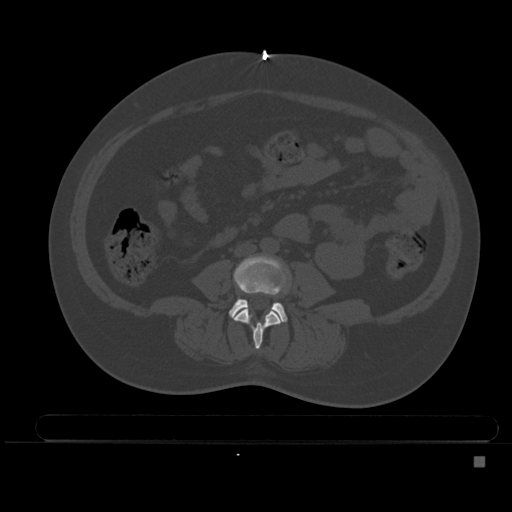
CT including the spine, one axial slice; slice 139 of 495 in the series (ordered by position); bone window (W 1800 / L 400 HU); 1.5 mm slice thickness; 512 × 512 image matrix, field of view 404 × 404 mm. Patient: female, 33 years. Case-level facts recorded for this patient, not image findings: primary cancer: breast; vertebrae with lytic lesions (as recorded): T1.
Annotated regions visible in this slice (semi-automatically segmented with operator editing):
- L3 vertebra: bounding box (x1, y1, x2, y2) in pixels: (234, 307, 282, 349)
- L4 vertebra: (229, 256, 287, 322)